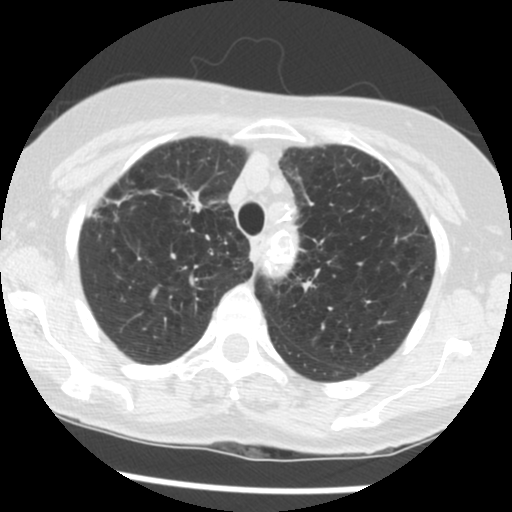
Low-dose screening chest CT, one axial slice; reconstruction kernel STANDARD; 120 kVp; lung window (W 1500 / L -600 HU); 512 × 512 image matrix, field of view 290 × 290 mm.
Structures marked on this image (outlined manually by an expert reader):
- lesion 1 (tumor, upper lobe of right lung): bounding box [x1, y1, x2, y2] px = [189, 191, 202, 212]